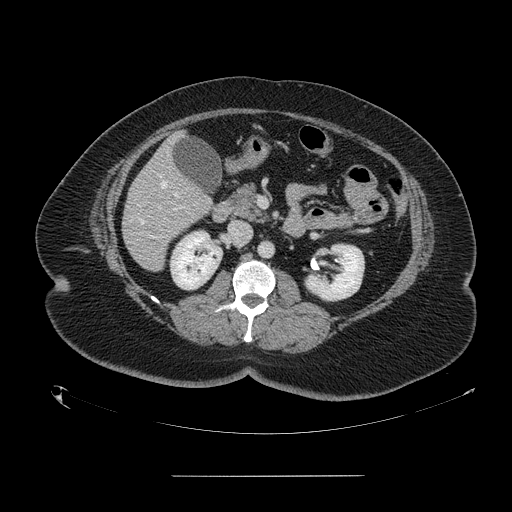
Contrast-enhanced abdominal CT, one axial slice; slice 63 of 164 in the series (ordered by position); soft-tissue window (W 400 / L 40 HU); 2.5 mm slice thickness; 512 × 512 image matrix, field of view 495 × 495 mm. Female patient, age 52 years. Case-level facts recorded for this patient, not image findings: diagnosis: colorectal cancer liver metastases, imaged before liver resection; multiple liver metastases: yes; largest metastasis: 3.5 cm.
Structures marked on this image (expert manual segmentation):
- hepatic veins: bounding box [x1, y1, x2, y2] px = [138, 181, 178, 235]
- liver: [123, 136, 212, 271]
- portal vein (with intrahepatic branches): [174, 194, 177, 197]